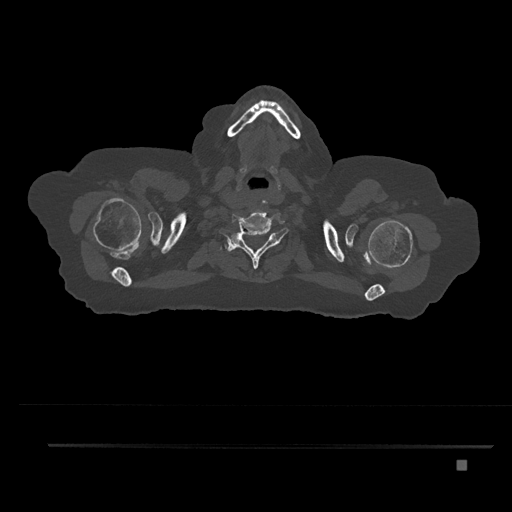
CT including the spine, one axial slice; slice 726 of 797 in the series (ordered by position); bone window (W 1800 / L 400 HU); 0.5 mm slice thickness; 512 × 512 image matrix, field of view 437 × 437 mm. Patient: female, 76 years. From the clinical record (not read from this slice): primary cancer: lung; vertebrae with lytic lesions (as recorded): T11, L3.
Annotated regions visible in this slice (semi-automatically segmented with operator editing):
- T1 vertebra: bounding box (x1, y1, x2, y2) in pixels: (228, 241, 252, 255)